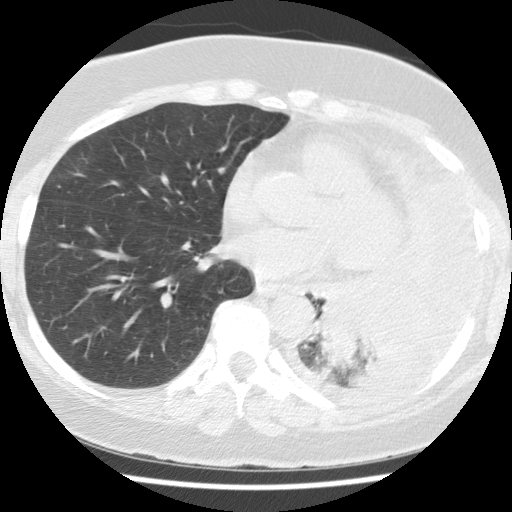
Axial slice from a low-dose chest CT screening exam. First (baseline) screen. Lung window (W 1500 / L -600 HU). Standard (soft-tissue) reconstruction kernel (STANDARD). 120 kVp. Slice 67 of 114 in the series. 512 × 512 image matrix. Female, age 65 years at enrolment. Current smoker at enrolment.
Expert-annotated lung lesion, bounding box (x1, y1, x2, y2) in pixels: (311, 282, 429, 380). Screening reader's record for this exam (one nodule recorded; not confirmed to be the boxed lesion): non-calcified nodule or mass ≥4 mm, left lower lobe, 74 × 48 mm, spiculated (stellate) margins, soft tissue attenuation. Participant outcome: lung cancer diagnosed 13 days after this screen — adenocarcinoma, NOS, left lower lobe, stage IV (AJCC 6th edition), 74 mm at pathology.